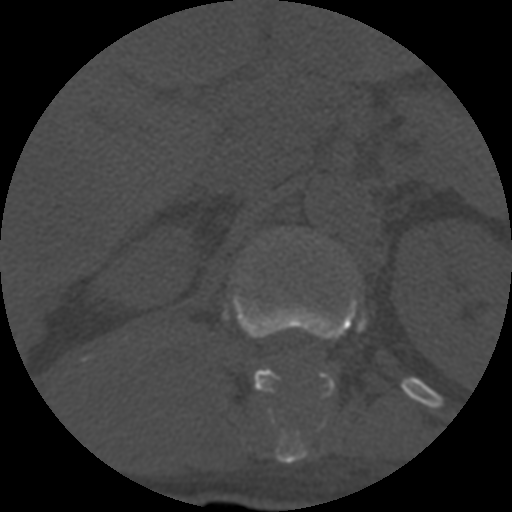
CT including the spine, one axial slice; one of 3 acquisitions stored at this slice position; bone window (W 1800 / L 400 HU); 1.25 mm slice thickness; 512 × 512 image matrix, field of view 160 × 160 mm. Patient age 55 years. Case-level facts recorded for this patient, not image findings: primary cancer: colon.
Structures marked on this image (semi-automatic segmentation, software-assisted and operator-edited):
- L1 vertebra: bounding box <330,387,334,393> (left, top, right, bottom; pixels)
- T12 vertebra: <223,290,367,464>